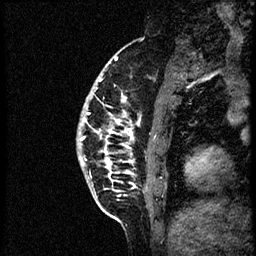
Breast MRI (dynamic contrast-enhanced), one sagittal slice; position 13 of 56 along the scan axis; dynamic contrast-enhanced study with each time point stored as its own series, time point 2 of 3 at this slice position (early post-contrast, ordered by acquisition time); 1.5 T; TE 4.2 ms, TR 21.3 ms; 256 × 256 image matrix, field of view 200 × 200 mm. Female patient, age 41 years. Case-level facts recorded for this patient, not image findings: setting: breast cancer imaged before/during neoadjuvant chemotherapy; receptor status: HER2-positive.
Annotated regions visible in this slice (semi-automatic segmentation, software-assisted and operator-edited):
- analysis volume of interest (the breast-tissue region the enhancement analysis was run in; not a lesion): box from (x=76, y=73) to (x=177, y=205) px
- tumour enhancement mask (voxels above the 100 % enhancement threshold inside the analysis volume of interest): (x=80, y=78)–(x=133, y=176)